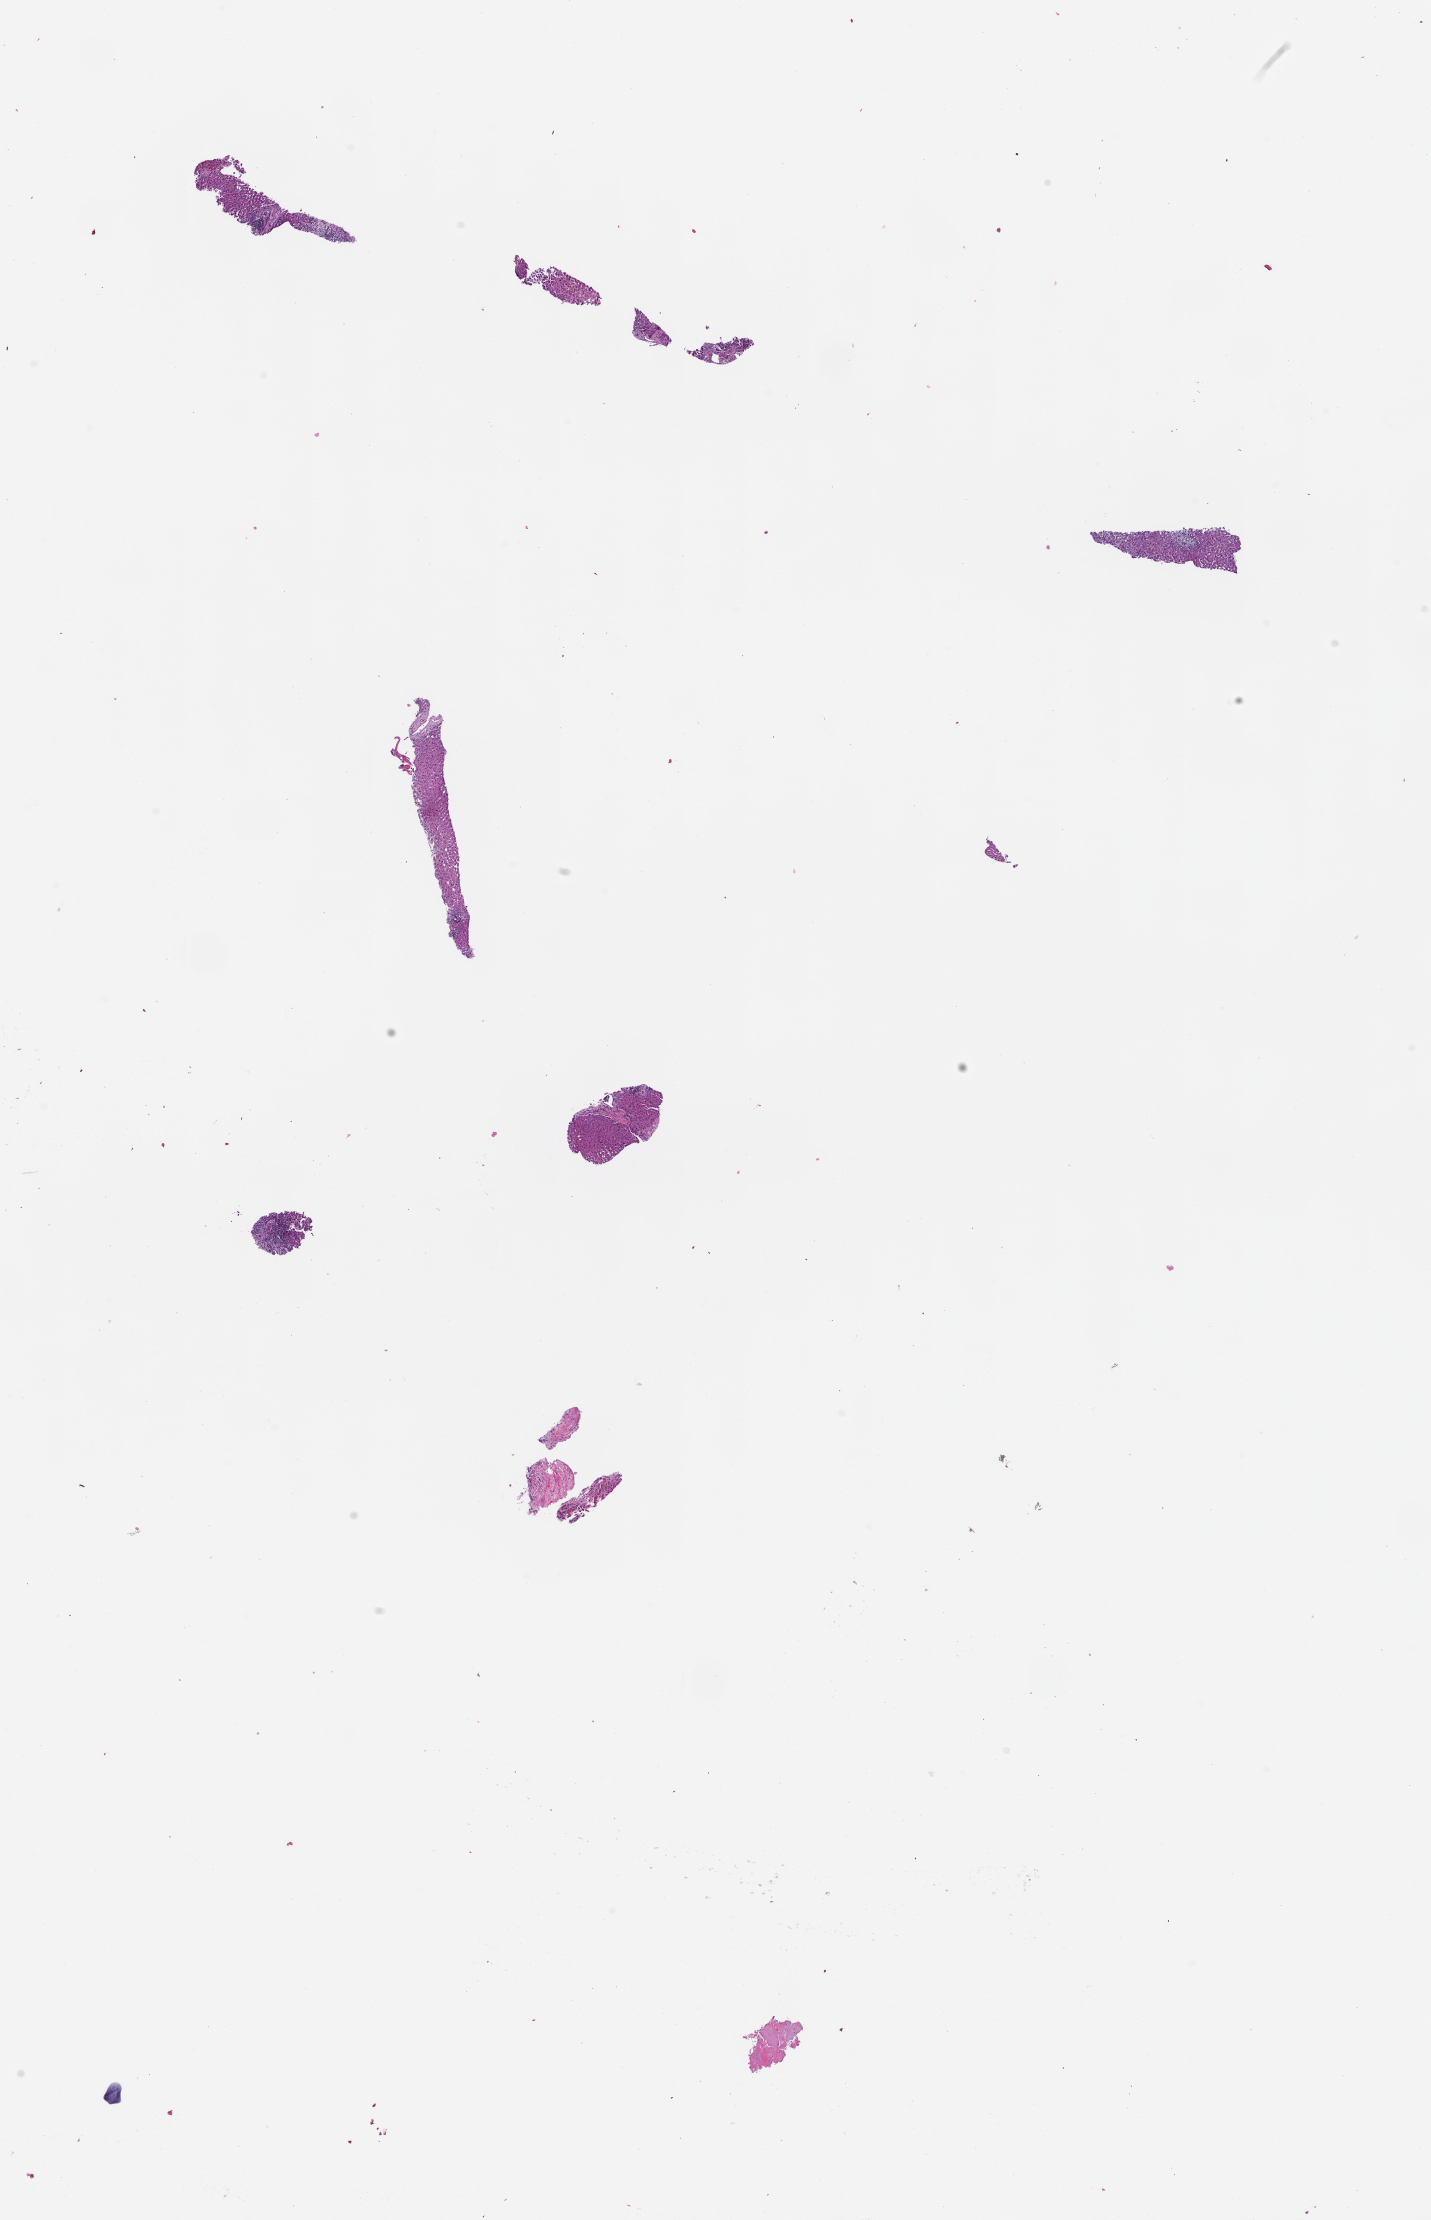
Digitized H&E-stained section — low-resolution overview of the scanned area, about 11.6 x 17.9 mm; formalin-fixed, paraffin-embedded (FFPE) tissue; specimen time point: archival tissue. Male patient.
This section: metastatic tumor tissue. Primary diagnosis of the patient: Colorectal Carcinoma.